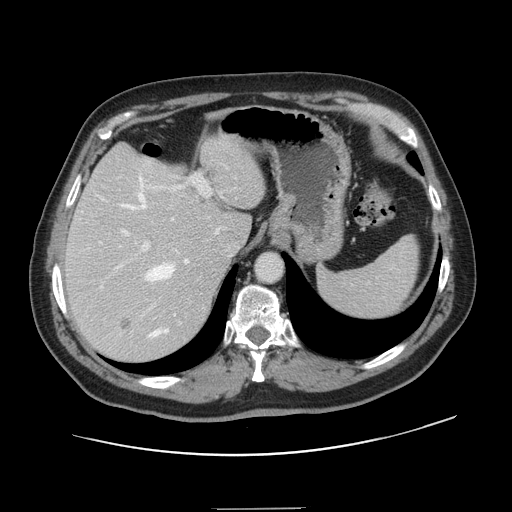
Contrast-enhanced abdominal CT, one axial slice. Position 105 of 143 along the scan axis. 120 kVp. Intravenous contrast given. Soft-tissue window (W 400 / L 40 HU). 512 × 512 image matrix. Male patient, age 62 years. Case-level facts recorded for this patient, not image findings: diagnosis: colorectal cancer liver metastases, imaged before liver resection; multiple liver metastases: yes; largest metastasis: 2.7 cm; disease in both lobes: no.
Outlined on this slice (expert manual segmentation):
- hepatic veins: bounding box (x1, y1, x2, y2) in pixels: (100, 176, 189, 338)
- liver: (66, 136, 265, 360)
- planned liver remnant (the part of the liver to remain after resection): (67, 136, 264, 269)
- portal vein (with intrahepatic branches): (101, 173, 211, 288)
- liver metastasis: (119, 320, 133, 331)